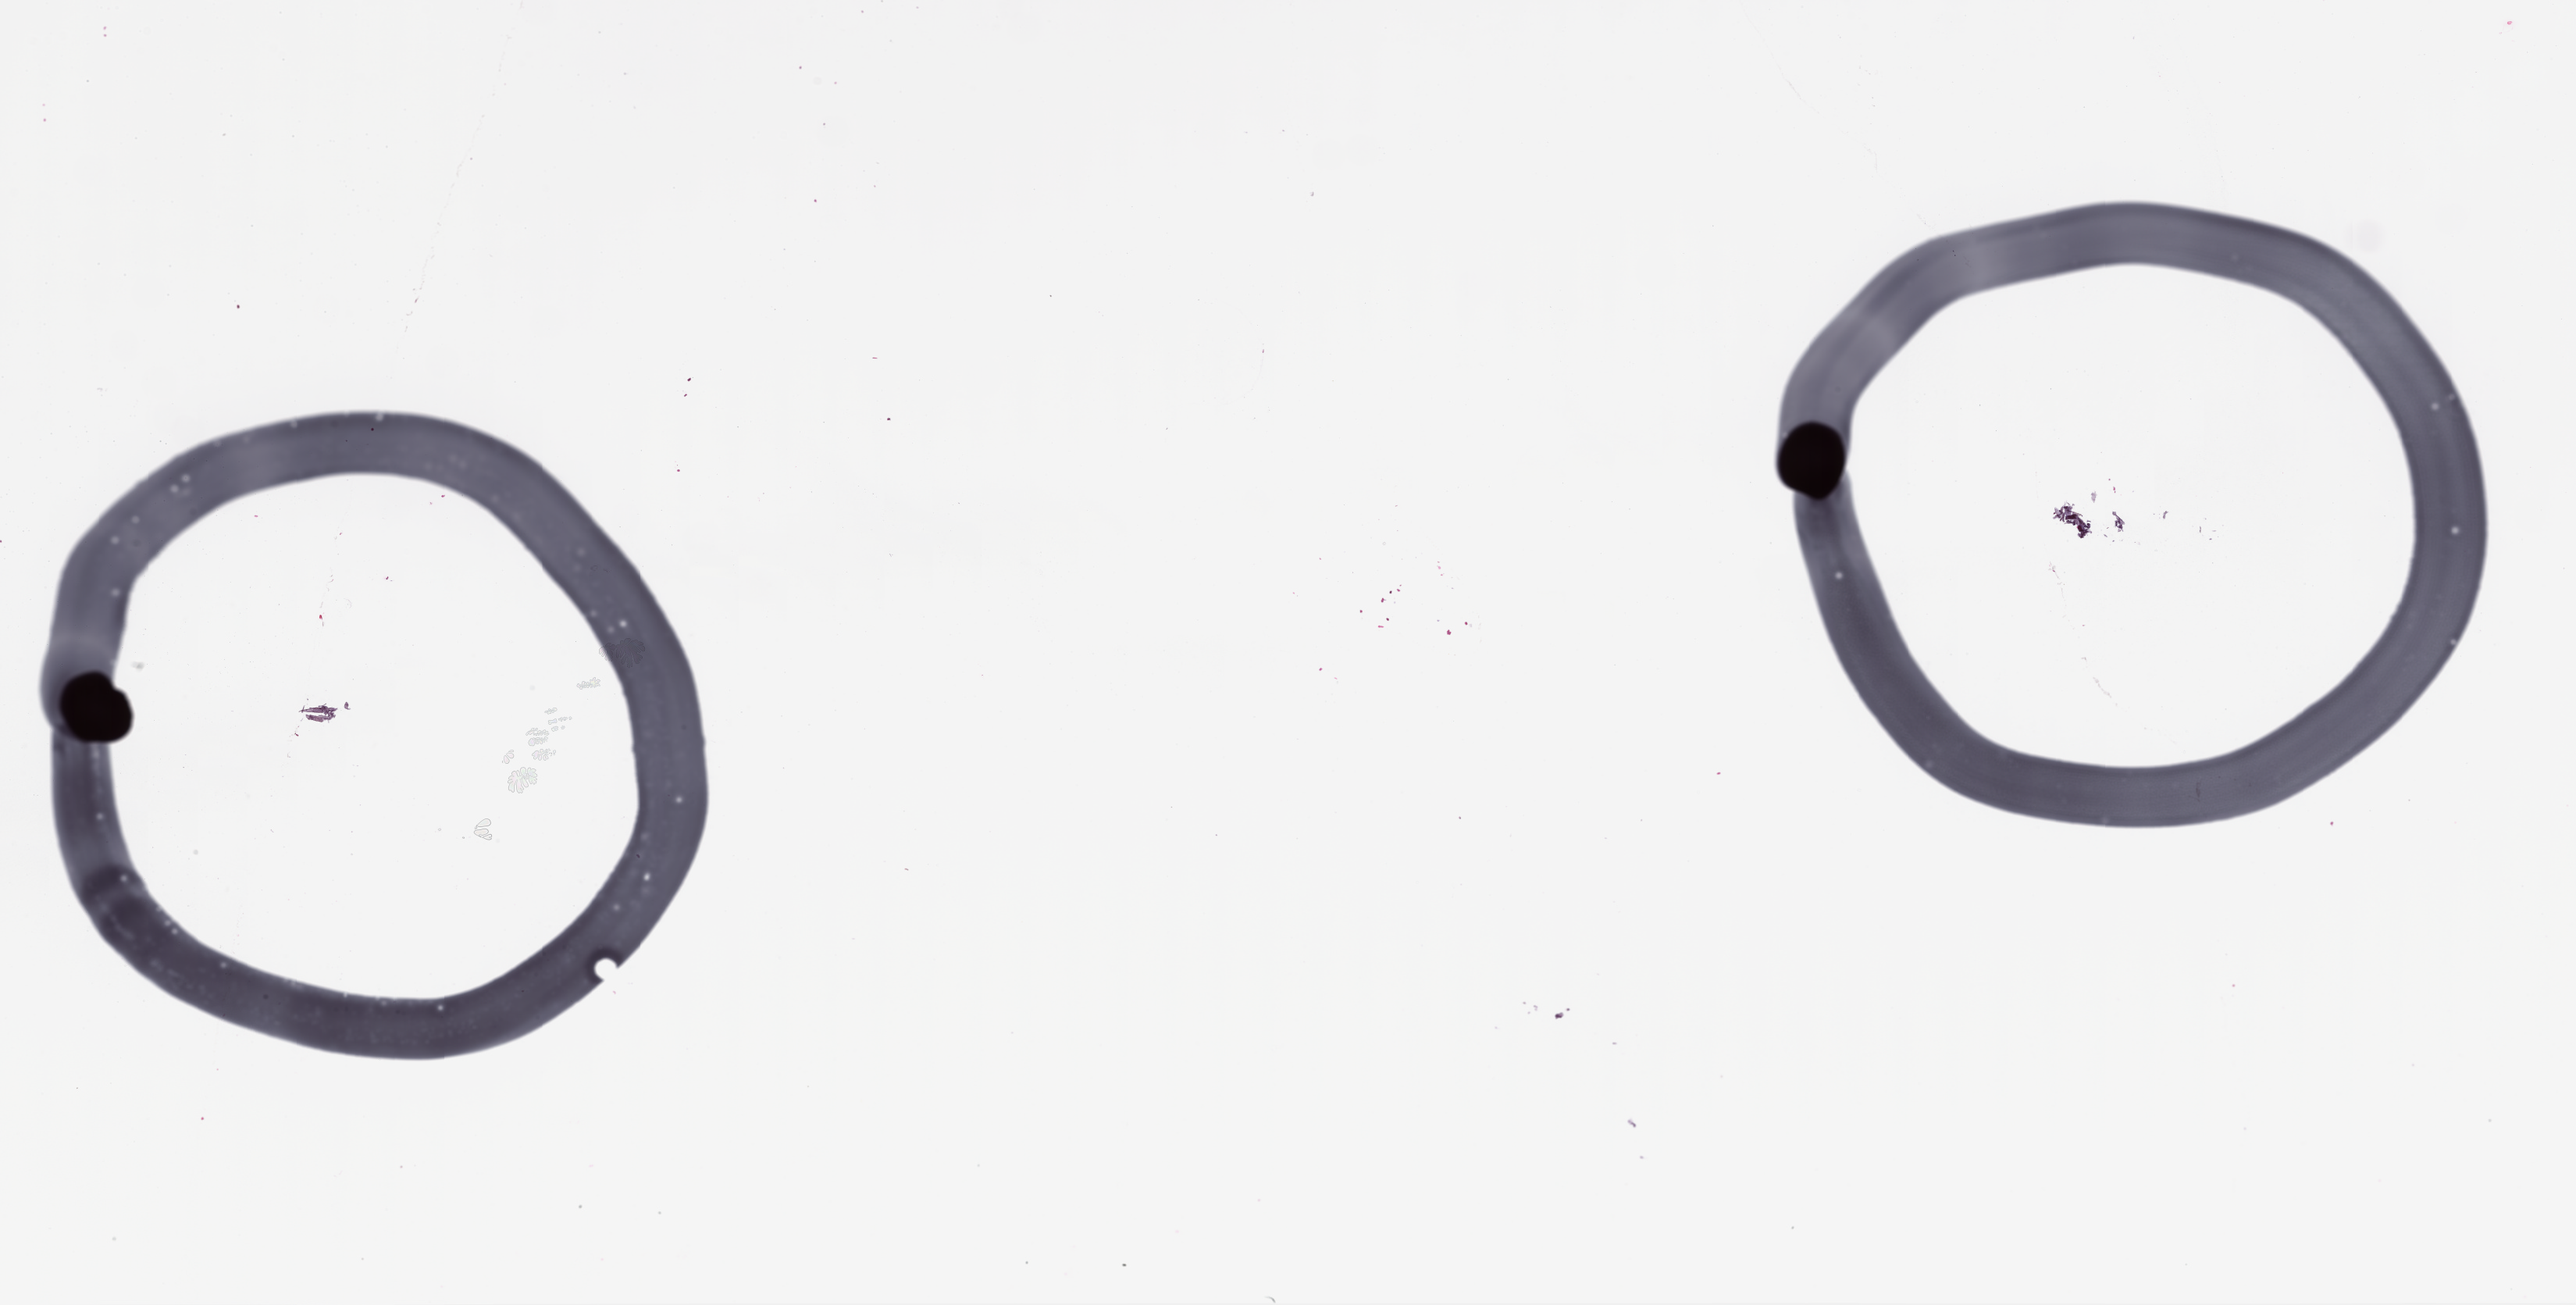
Whole-slide image, haematoxylin and eosin stain — whole scanned area (about 26.6 x 13.5 mm) shown as a low-resolution overview. FFPE section. Tissue site: lung. Archival tissue. Male patient.
• this section: primary tumour tissue
• diagnosis: Non-Small Cell Lung Carcinoma